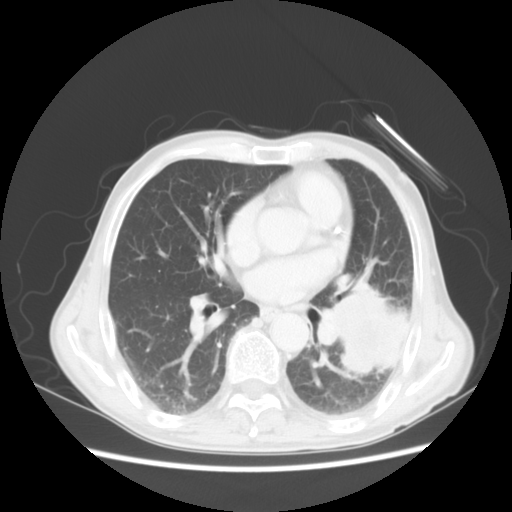
Chest CT, one axial slice; slice 25 of 51 in the series (ordered by position); reconstruction kernel STANDARD; 120 kVp; lung window (W 1500 / L -600 HU); 5 mm slice thickness; 512 × 512 image matrix, field of view 360 × 360 mm. Male patient, age 64 years. Case-level facts recorded for this patient, not image findings: clinical TNM (as recorded): T4 N0 M0; histopathological grade: G2-3.
Annotated regions visible in this slice (rectangle marked by the reading radiologist):
- lung tumour (recorded histology: squamous cell carcinoma): bounding box (x1, y1, x2, y2) in pixels: (313, 283, 410, 385)